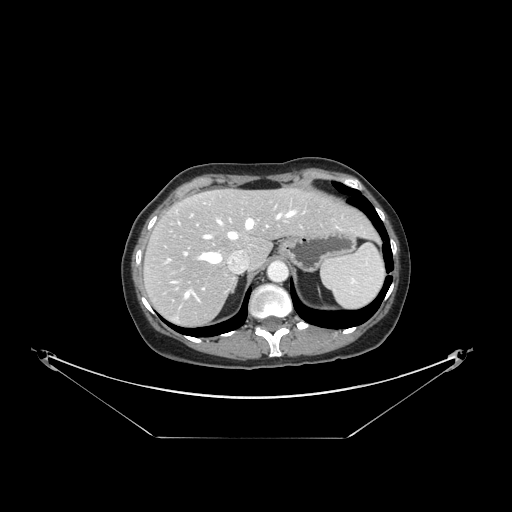
Contrast-enhanced abdominal CT, one axial slice. Slice 115 of 148 in the series (ordered by position). Reconstruction kernel STANDARD. 120 kVp. Intravenous contrast given. Soft-tissue window (W 400 / L 40 HU). 2.5 mm slice thickness. 512 × 512 image matrix, field of view 500 × 500 mm. Female patient, age 73 years. Case-level facts recorded for this patient, not image findings: diagnosis: colorectal cancer liver metastases, imaged before liver resection; multiple liver metastases: no; largest metastasis: 1 cm; chemotherapy before resection: yes.
Annotated regions visible in this slice (expert manual segmentation):
- hepatic veins: box from (x=184, y=210) to (x=305, y=299) px
- liver: (x=145, y=190)–(x=374, y=325)
- planned liver remnant (the part of the liver to remain after resection): (x=169, y=190)–(x=374, y=265)
- portal vein (with intrahepatic branches): (x=184, y=214)–(x=205, y=290)